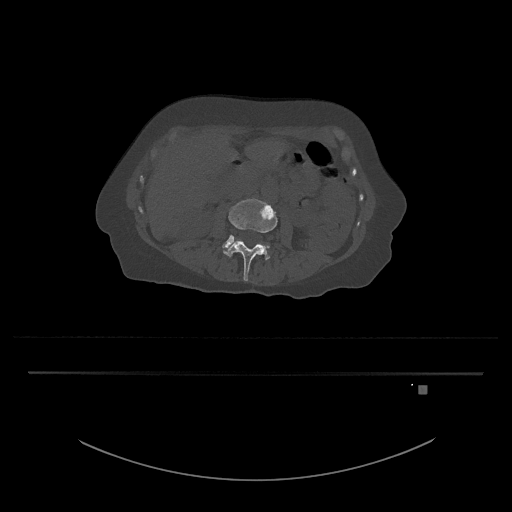
CT including the spine, one axial slice; position 414 of 797 along the scan axis; bone window (W 1800 / L 400 HU); 0.5 mm slice thickness; 512 × 512 image matrix, field of view 500 × 500 mm. Patient: female, 57 years. From the clinical record (not read from this slice): primary cancer: cervical.
Outlined on this slice (semi-automatic segmentation, software-assisted and operator-edited):
- L3 vertebra: box from (x=223, y=198) to (x=278, y=281) px
- L4 vertebra: (x=222, y=235)–(x=270, y=259)